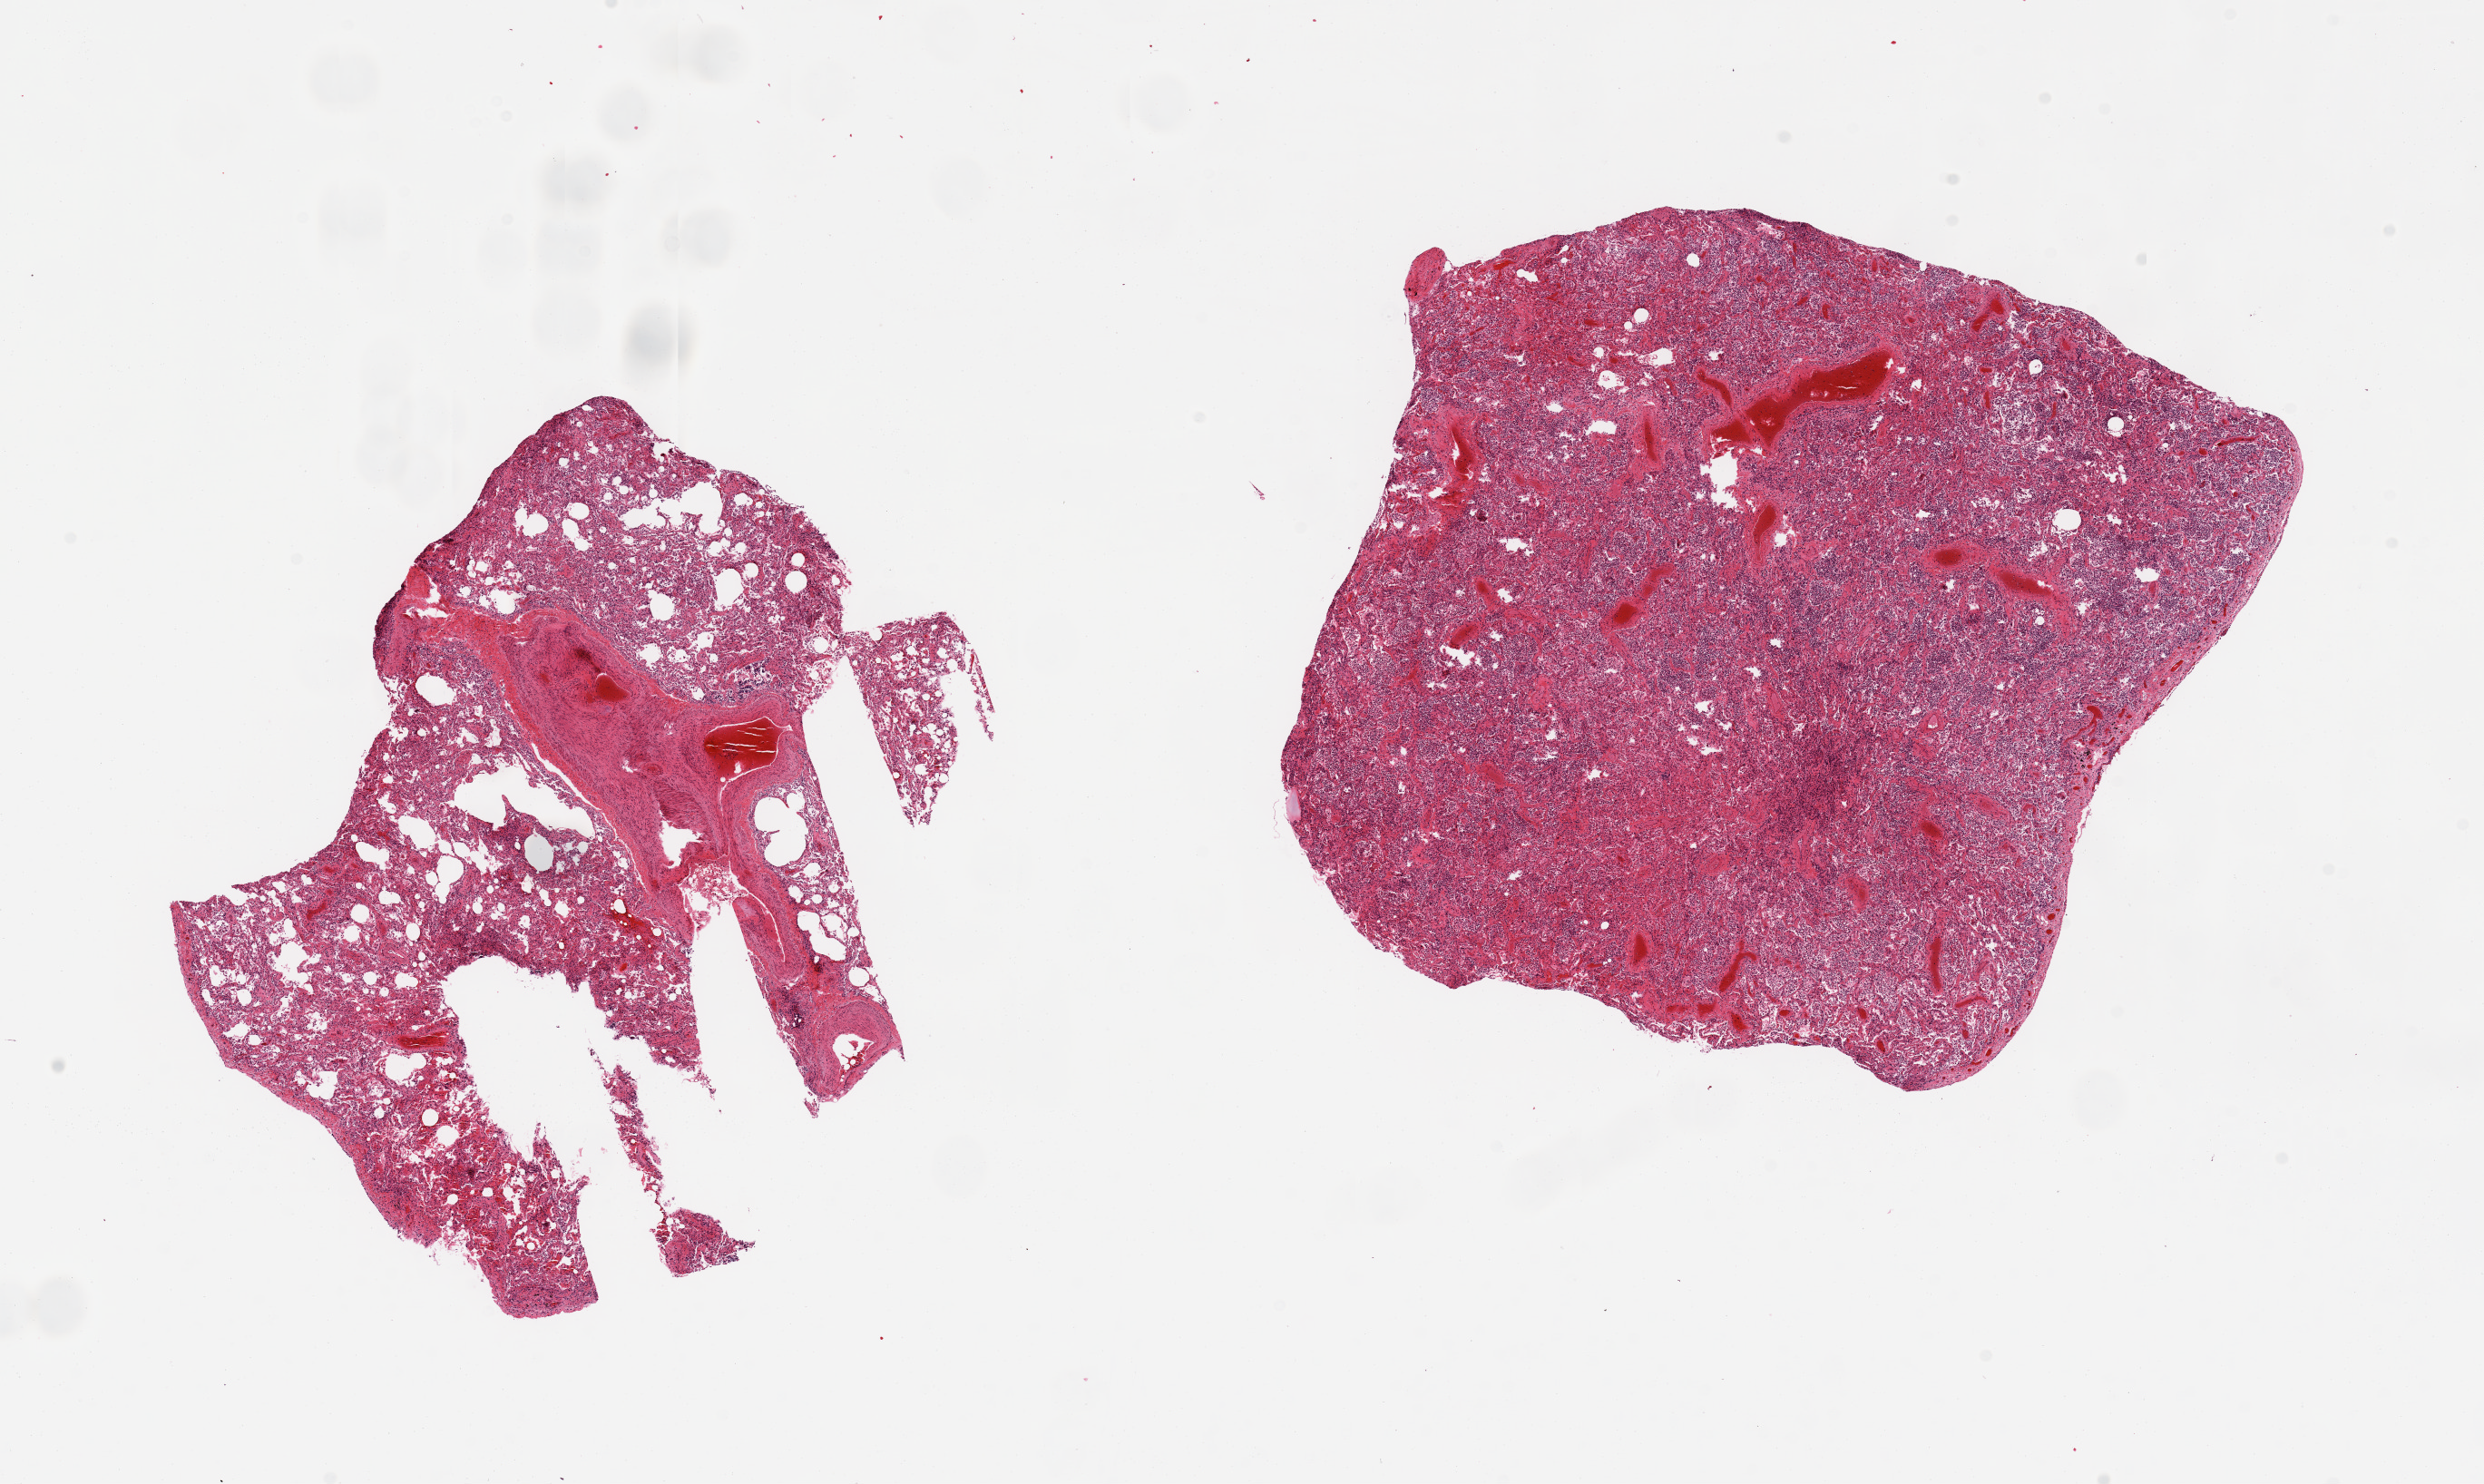
Haematoxylin and eosin whole-slide image, a low-resolution overview of the entire scanned area, about 21.7 x 12.9 mm (slide scanned at 20x). PAXgene-fixed paraffin-embedded (PFPE) section. Section of lung (target tissue). Tissue donor sample. Donor: female.
Pathologist's review note for this sample: 2 pieces; extensive pneumonia in one piece; fibrosis and patchy pneumonia in other.